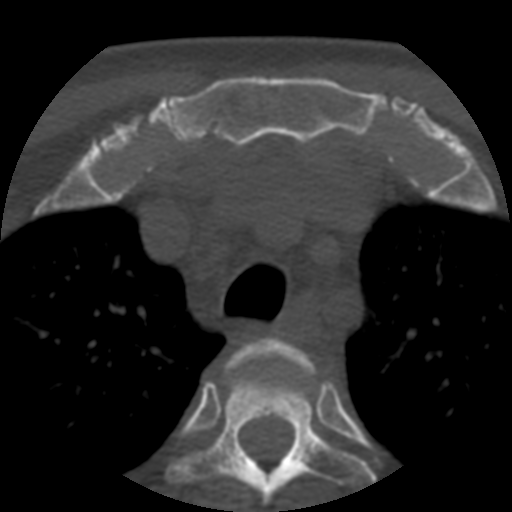
CT including the spine, one axial slice. Position 417 of 508 along the scan axis. Reconstruction kernel STANDARD. Bone window (W 1800 / L 400 HU). 1.25 mm slice thickness. 512 × 512 image matrix, field of view 160 × 160 mm. Patient age 57 years. Case-level facts recorded for this patient, not image findings: primary cancer: prostate.
Outlined on this slice (semi-automatically segmented with operator editing):
- T2 vertebra: bounding box (x1, y1, x2, y2) in pixels: (227, 338, 315, 380)
- T3 vertebra: (171, 350, 376, 505)